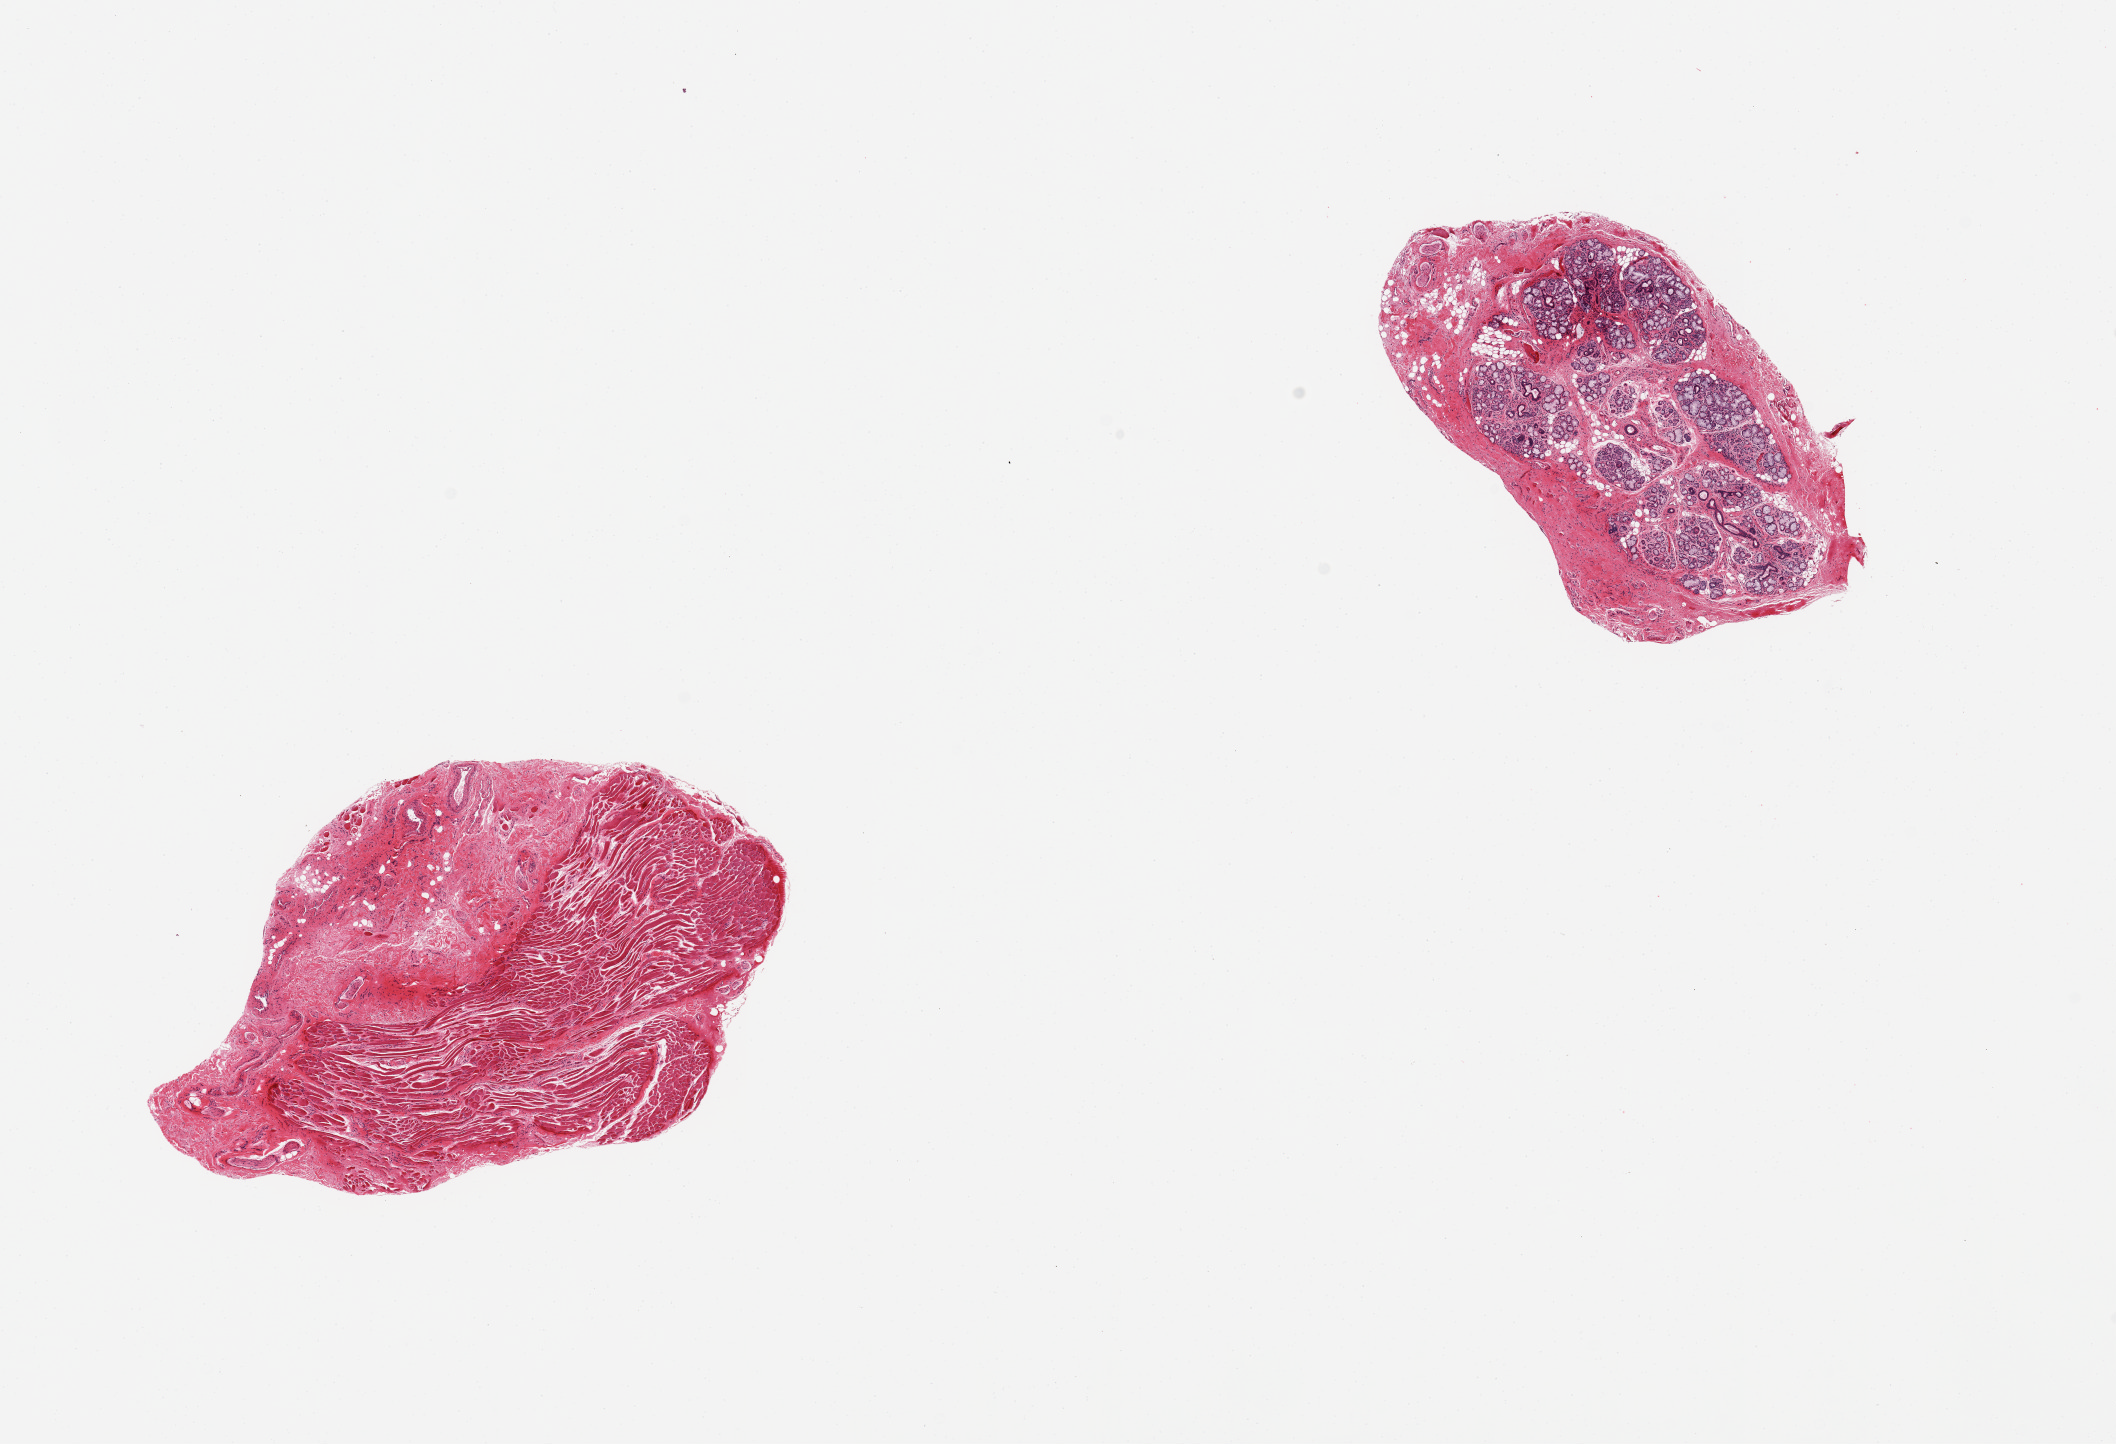
Digitized haematoxylin and eosin-stained section, low-resolution overview of the scanned area, about 16.7 x 11.4 mm. PAXgene-fixed paraffin-embedded (PFPE) section. Section of minor salivary gland (target tissue). Tissue donor sample. Male donor.
- reviewer comment on this tissue sample: 2 pieces; 1 piece is fibromuscular tissue, without glands